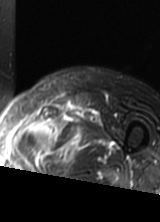
MRI of an extremity soft-tissue mass, one axial slice. Slice 49 of 69 in the series (ordered by position). T2-weighted fat-saturated. MR volume resampled by the dataset authors to the PET/CT grid (not the native acquisition matrix). 3.27 mm slice thickness. 160 × 222 image matrix. Female patient. From the clinical record (not read from this slice): histological type: pleomorphic leiomyosarcoma; grade: high; site of the primary tumour: left thigh.
Annotated regions visible in this slice (expert contour drawn on MRI and transferred to this co-registered scan by the dataset authors):
- gross tumour volume including surrounding oedema: bounding box [x1, y1, x2, y2] px = [16, 107, 80, 163]